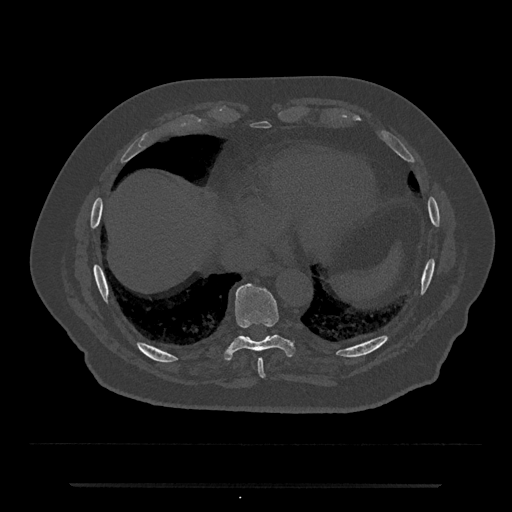
CT including the spine, one axial slice; position 757 of 797 along the scan axis; reconstruction kernel Br40s/3; 120 kVp; bone window (W 1800 / L 400 HU); 512 × 512 image matrix, field of view 434 × 434 mm. Patient: male, 80 years. From the clinical record (not read from this slice): primary cancer: prostate; vertebrae with lytic lesions (as recorded): L1, T11.
Structures marked on this image (semi-automatically segmented with operator editing):
- T8 vertebra: bounding box <257,359,265,378> (left, top, right, bottom; pixels)
- T9 vertebra: <225,283,294,360>